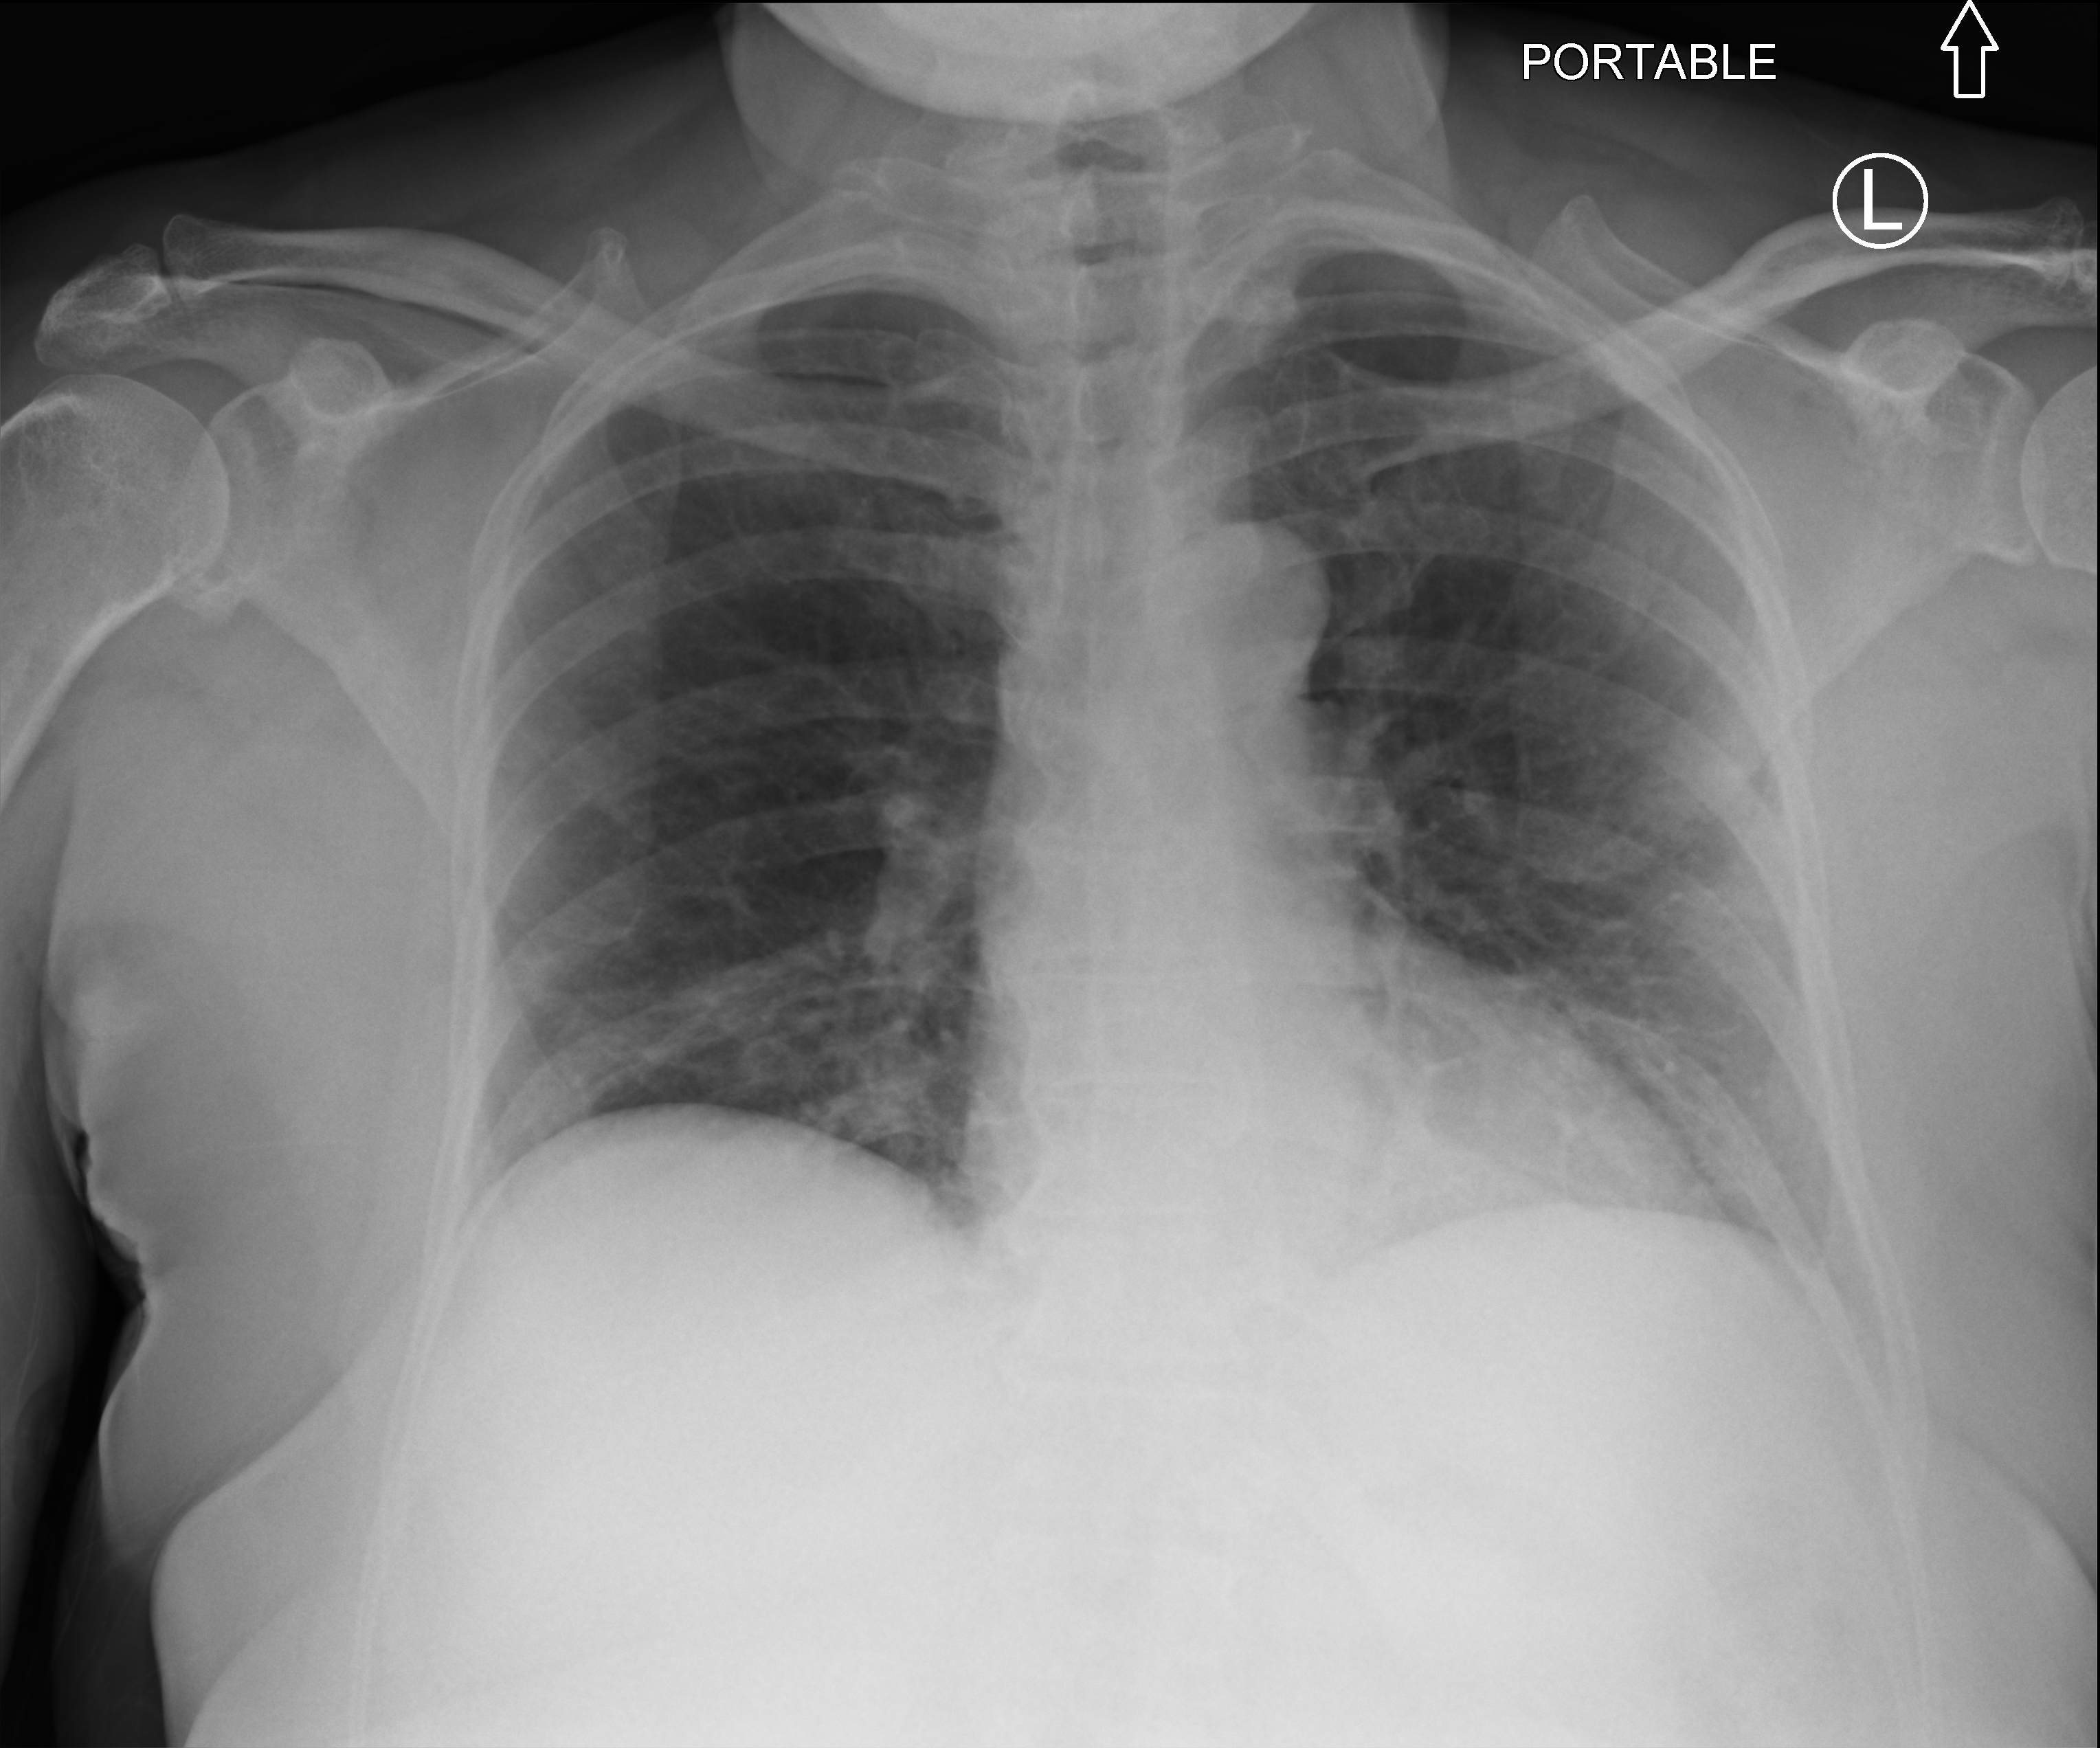
Bedside chest radiograph (computed radiography), anteroposterior (AP) projection. Patient hospitalised with COVID-19; female, aged 18–59 years.
Admission-level facts for this patient (not findings on this image; timing relative to this image not recorded):
- length of hospital stay: 1 day
- mechanically ventilated during this hospital stay: no
- admitted to intensive care during this hospital stay: no